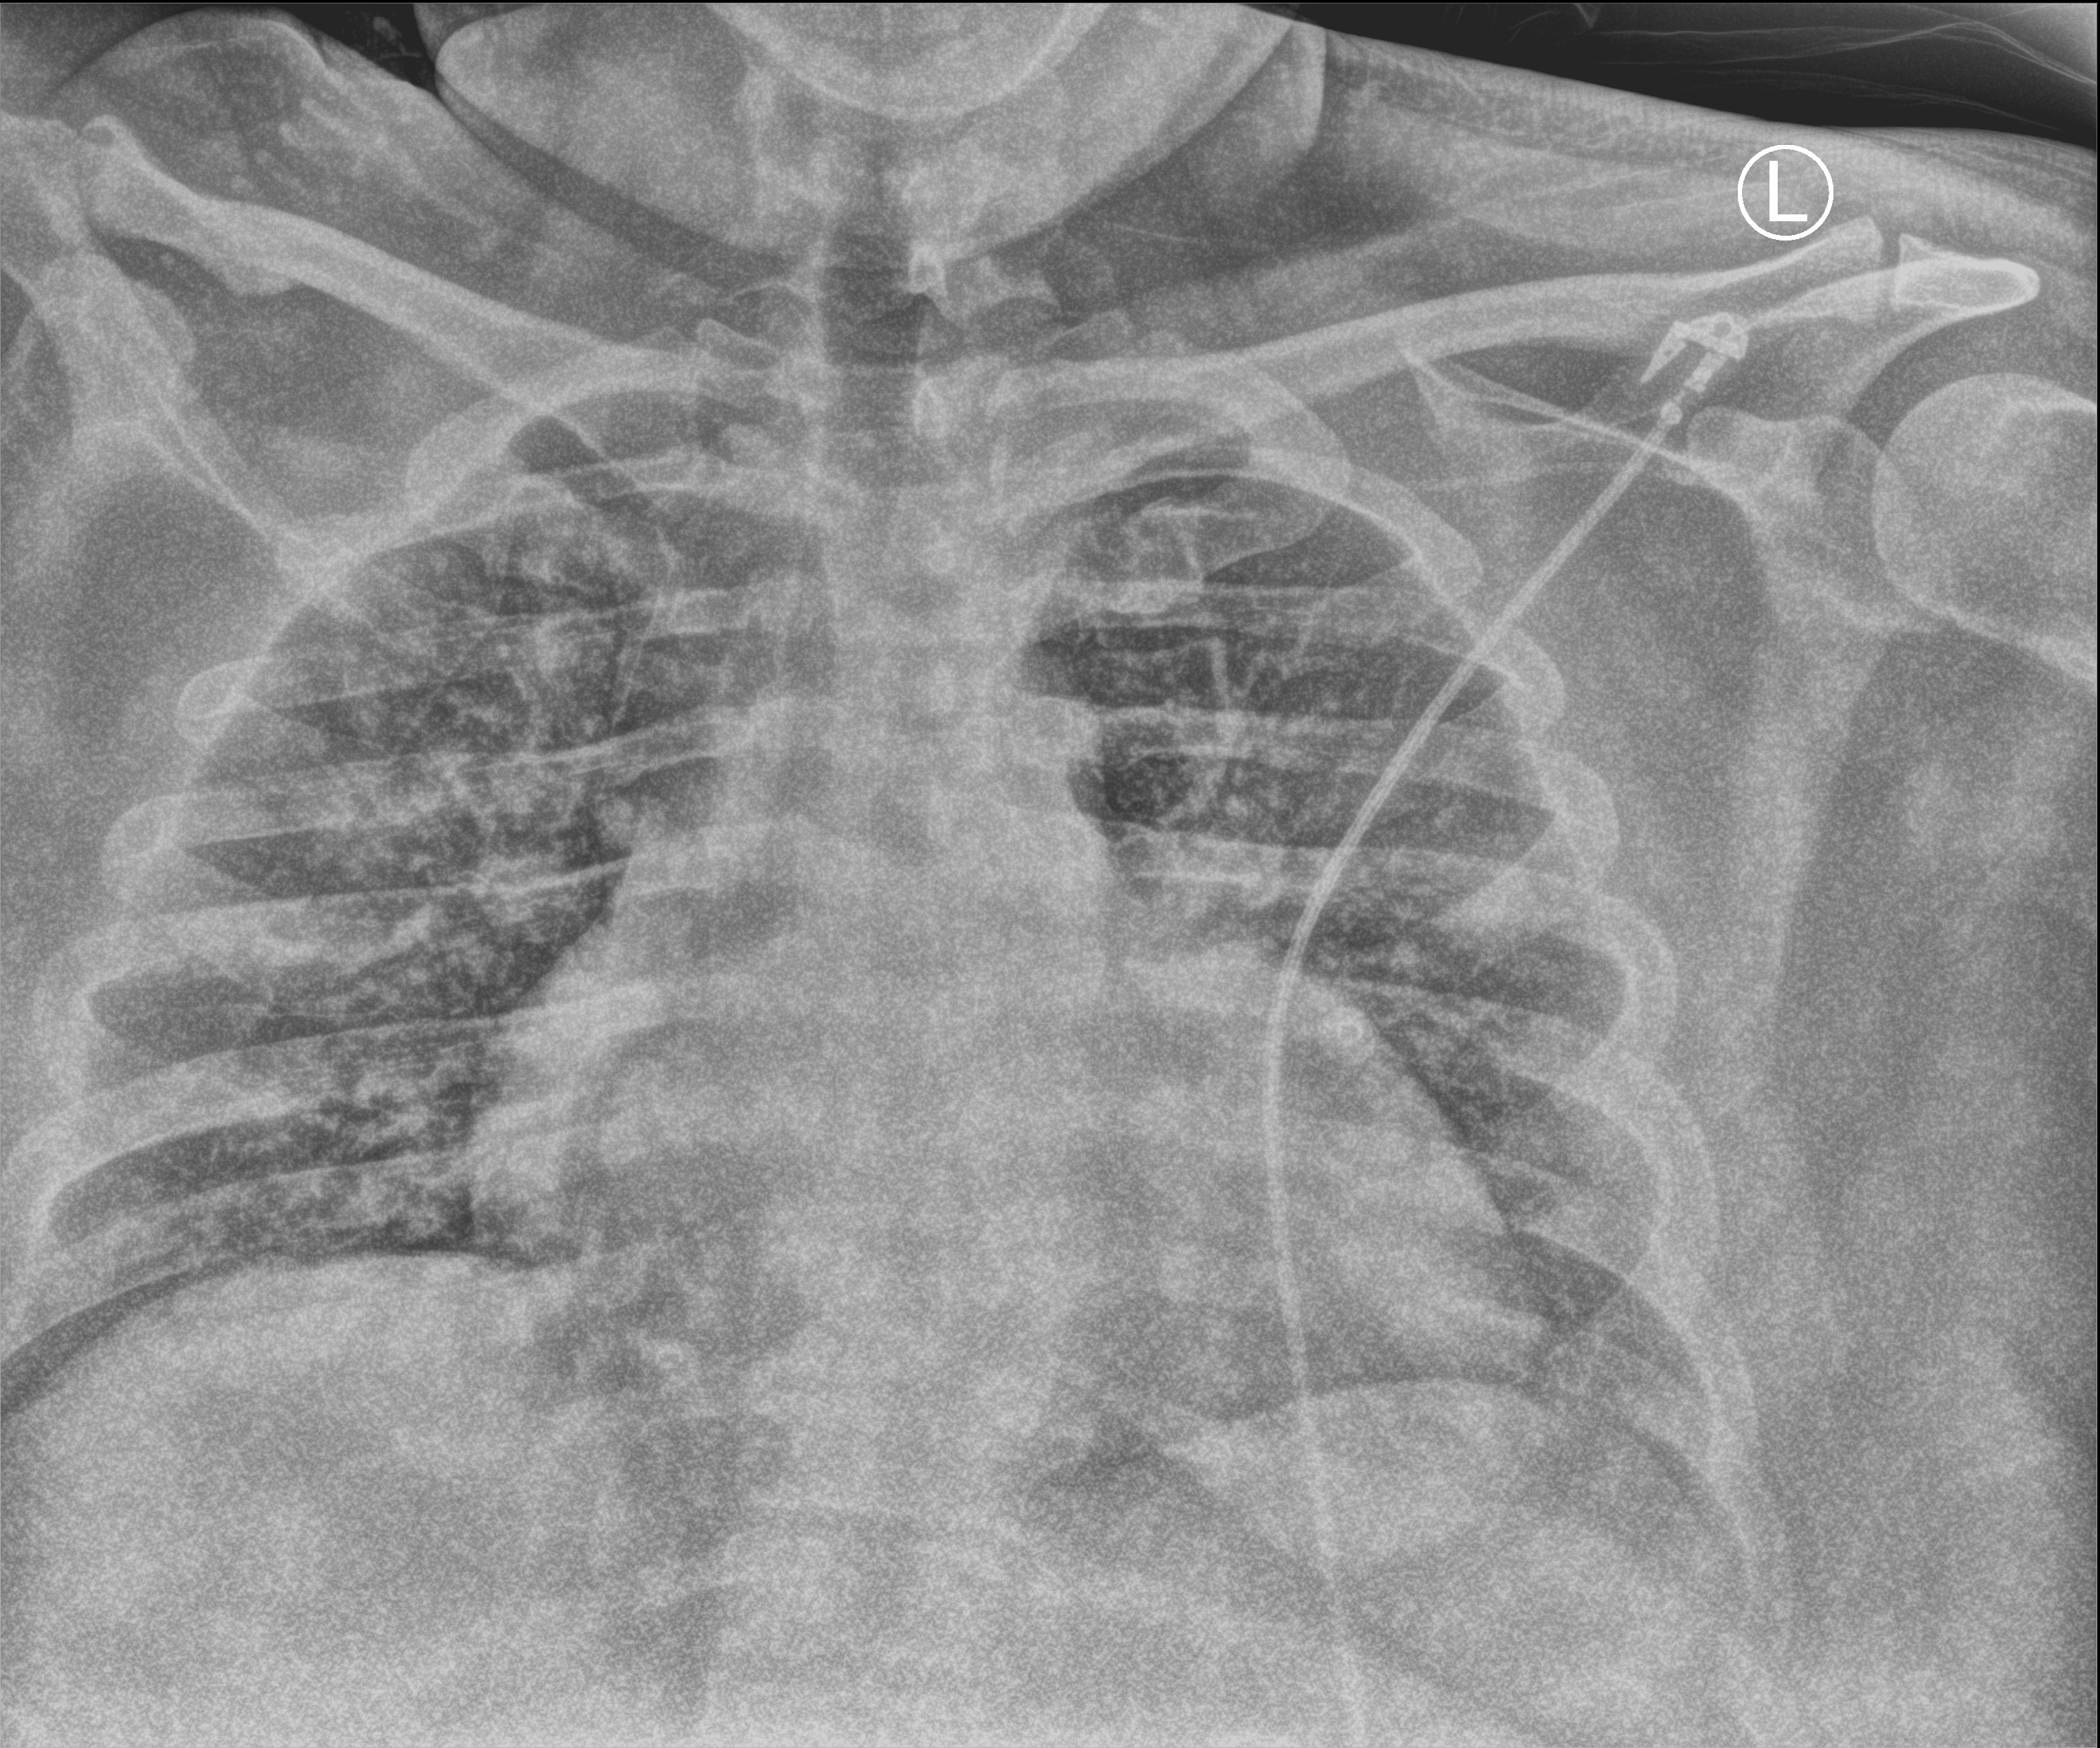
Portable chest radiograph. Male patient hospitalised with COVID-19, age 18–59 years.
Admission-level facts for this patient (not findings on this image; timing relative to this image not recorded): chronic kidney disease (admission record): no; hypertension (admission record): yes.